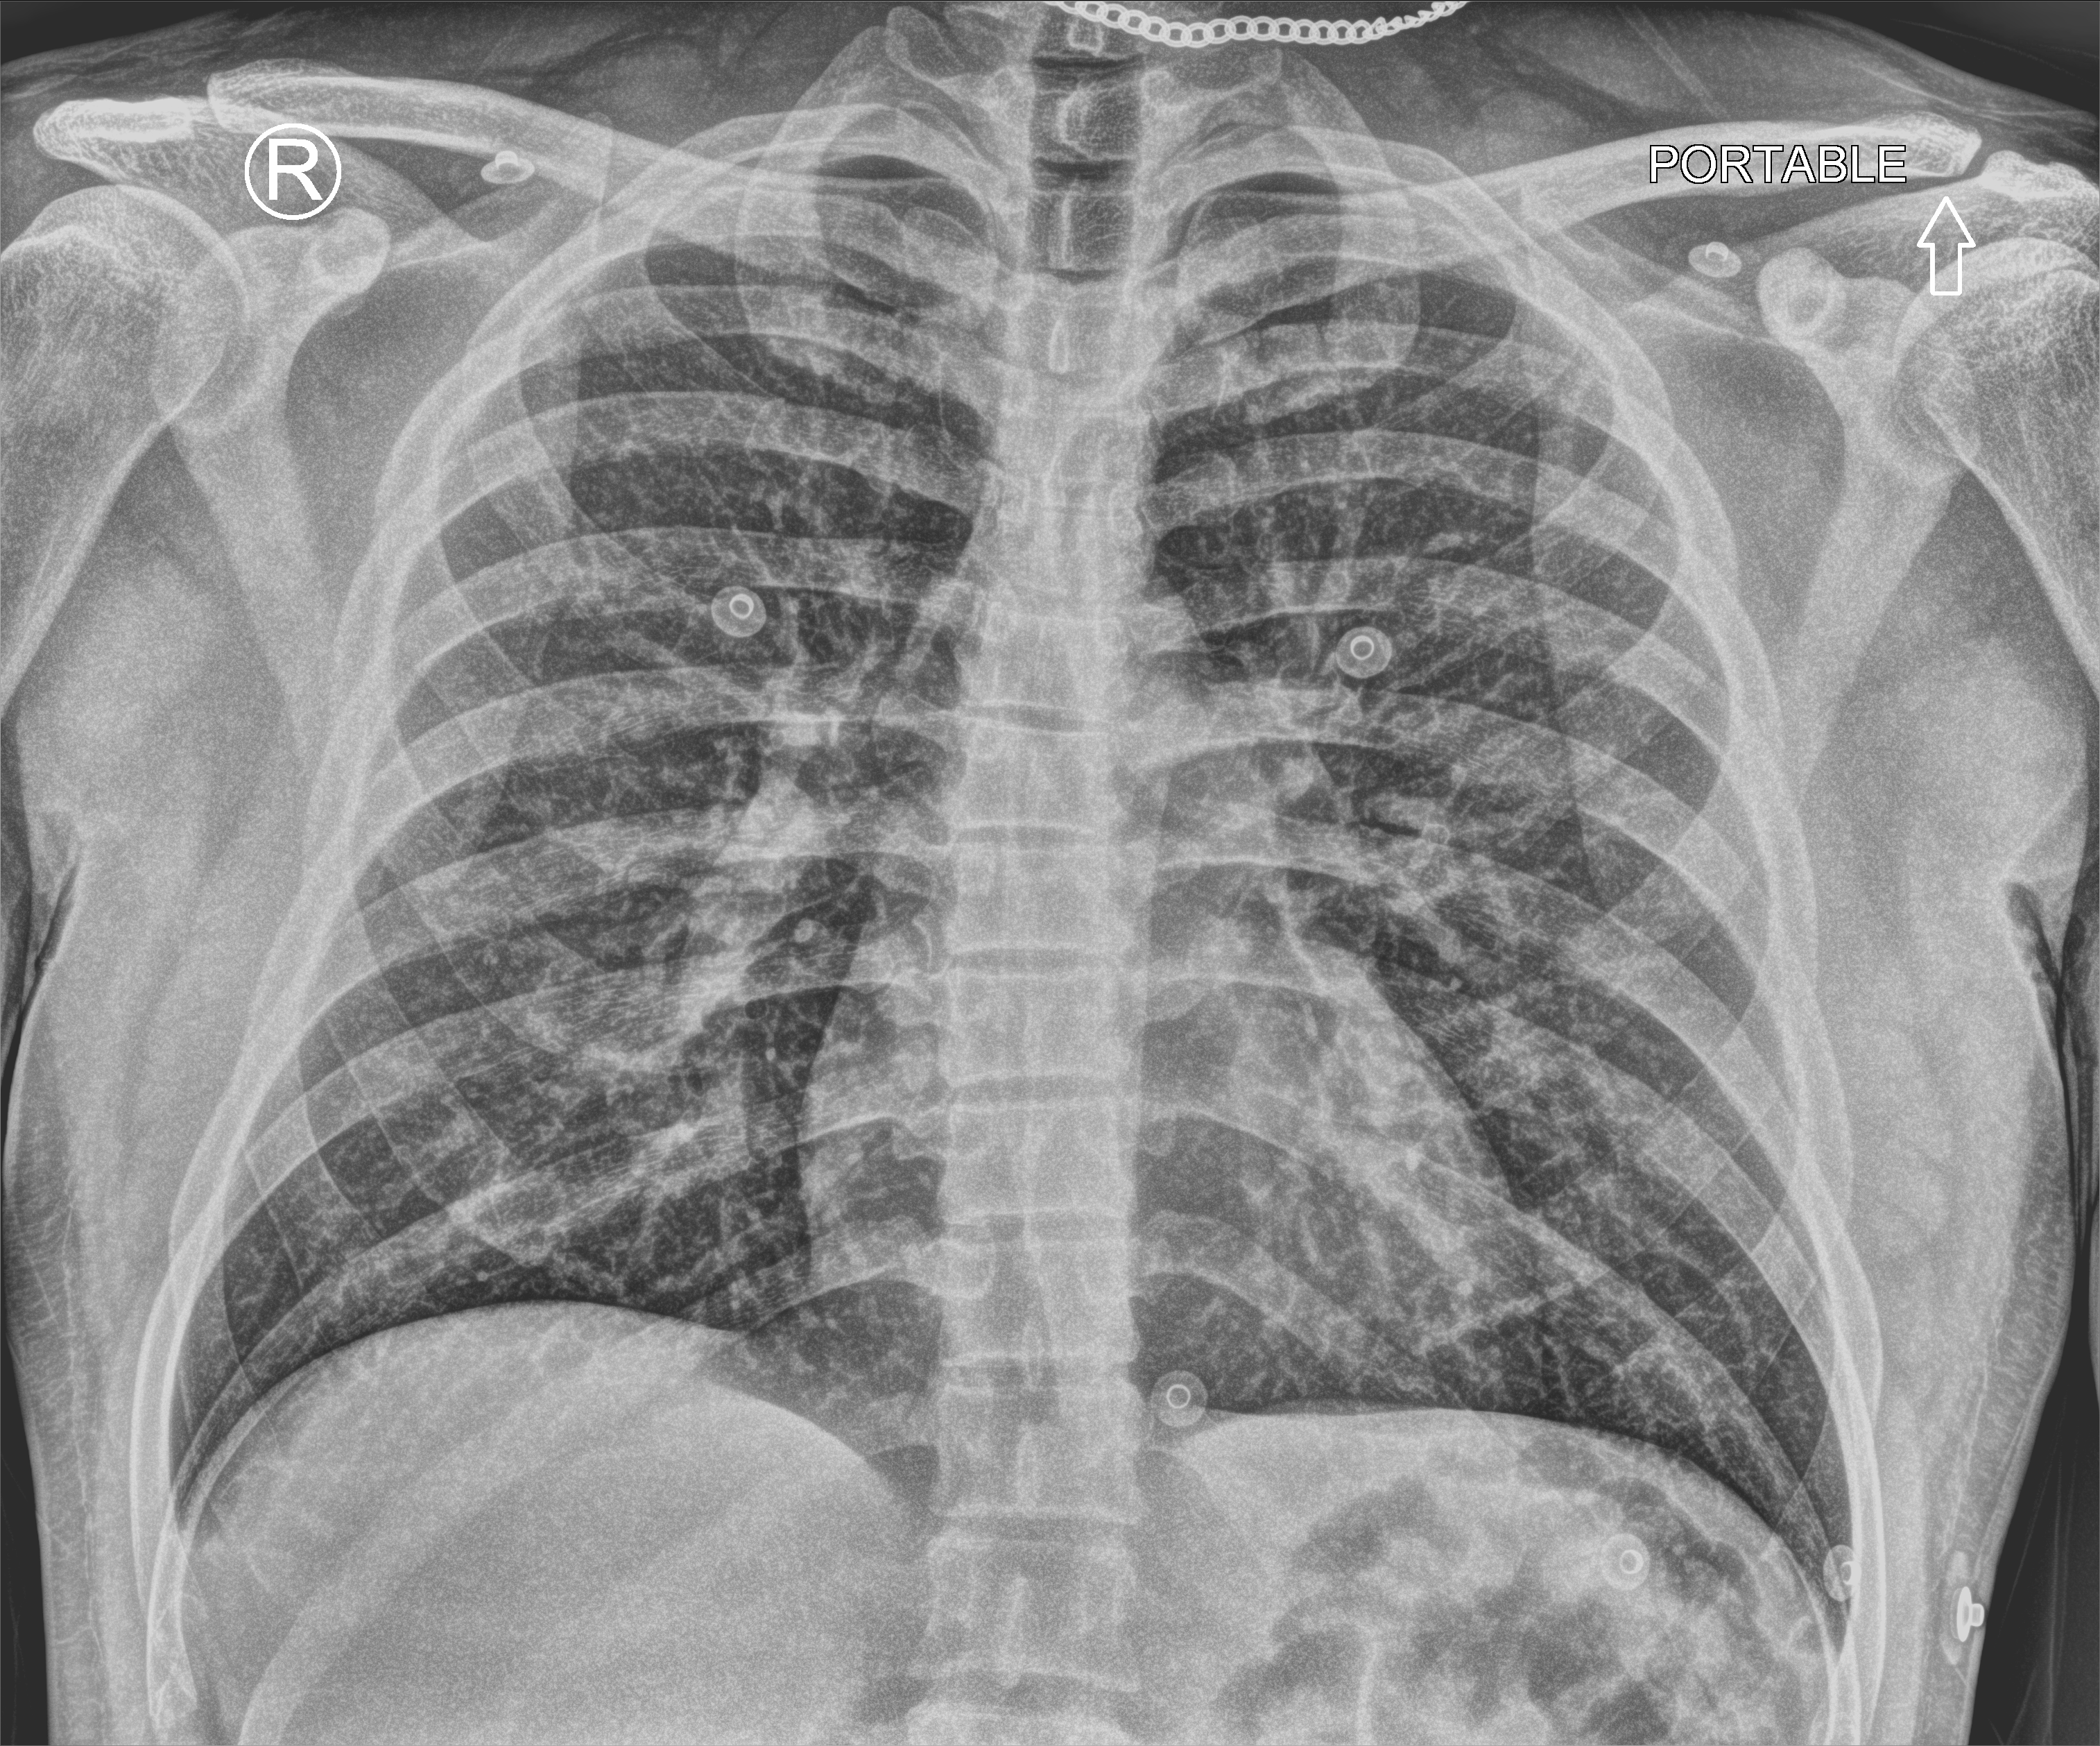
Portable chest radiograph. Male patient hospitalised with COVID-19, age 18–59 years.
Hospital-stay facts (about this admission, not read from this image; timing relative to this image not recorded):
- admitted to intensive care during this hospital stay: no